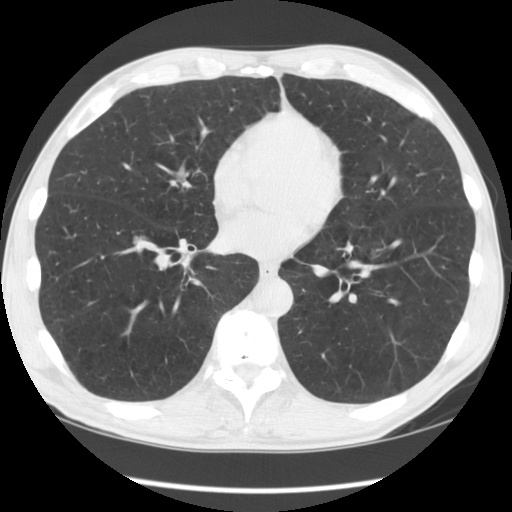
Low-dose screening chest CT, one axial slice; slice 49 of 135 in the series (ordered by position); reconstruction kernel STANDARD; 120 kVp; lung window (W 1500 / L -600 HU); 2.5 mm slice thickness; 512 × 512 image matrix.
Annotated regions visible in this slice (expert manual segmentation):
- lesion 1 (tumor, lower lobe of right lung): bounding box (x1, y1, x2, y2) in pixels: (134, 237, 149, 253)